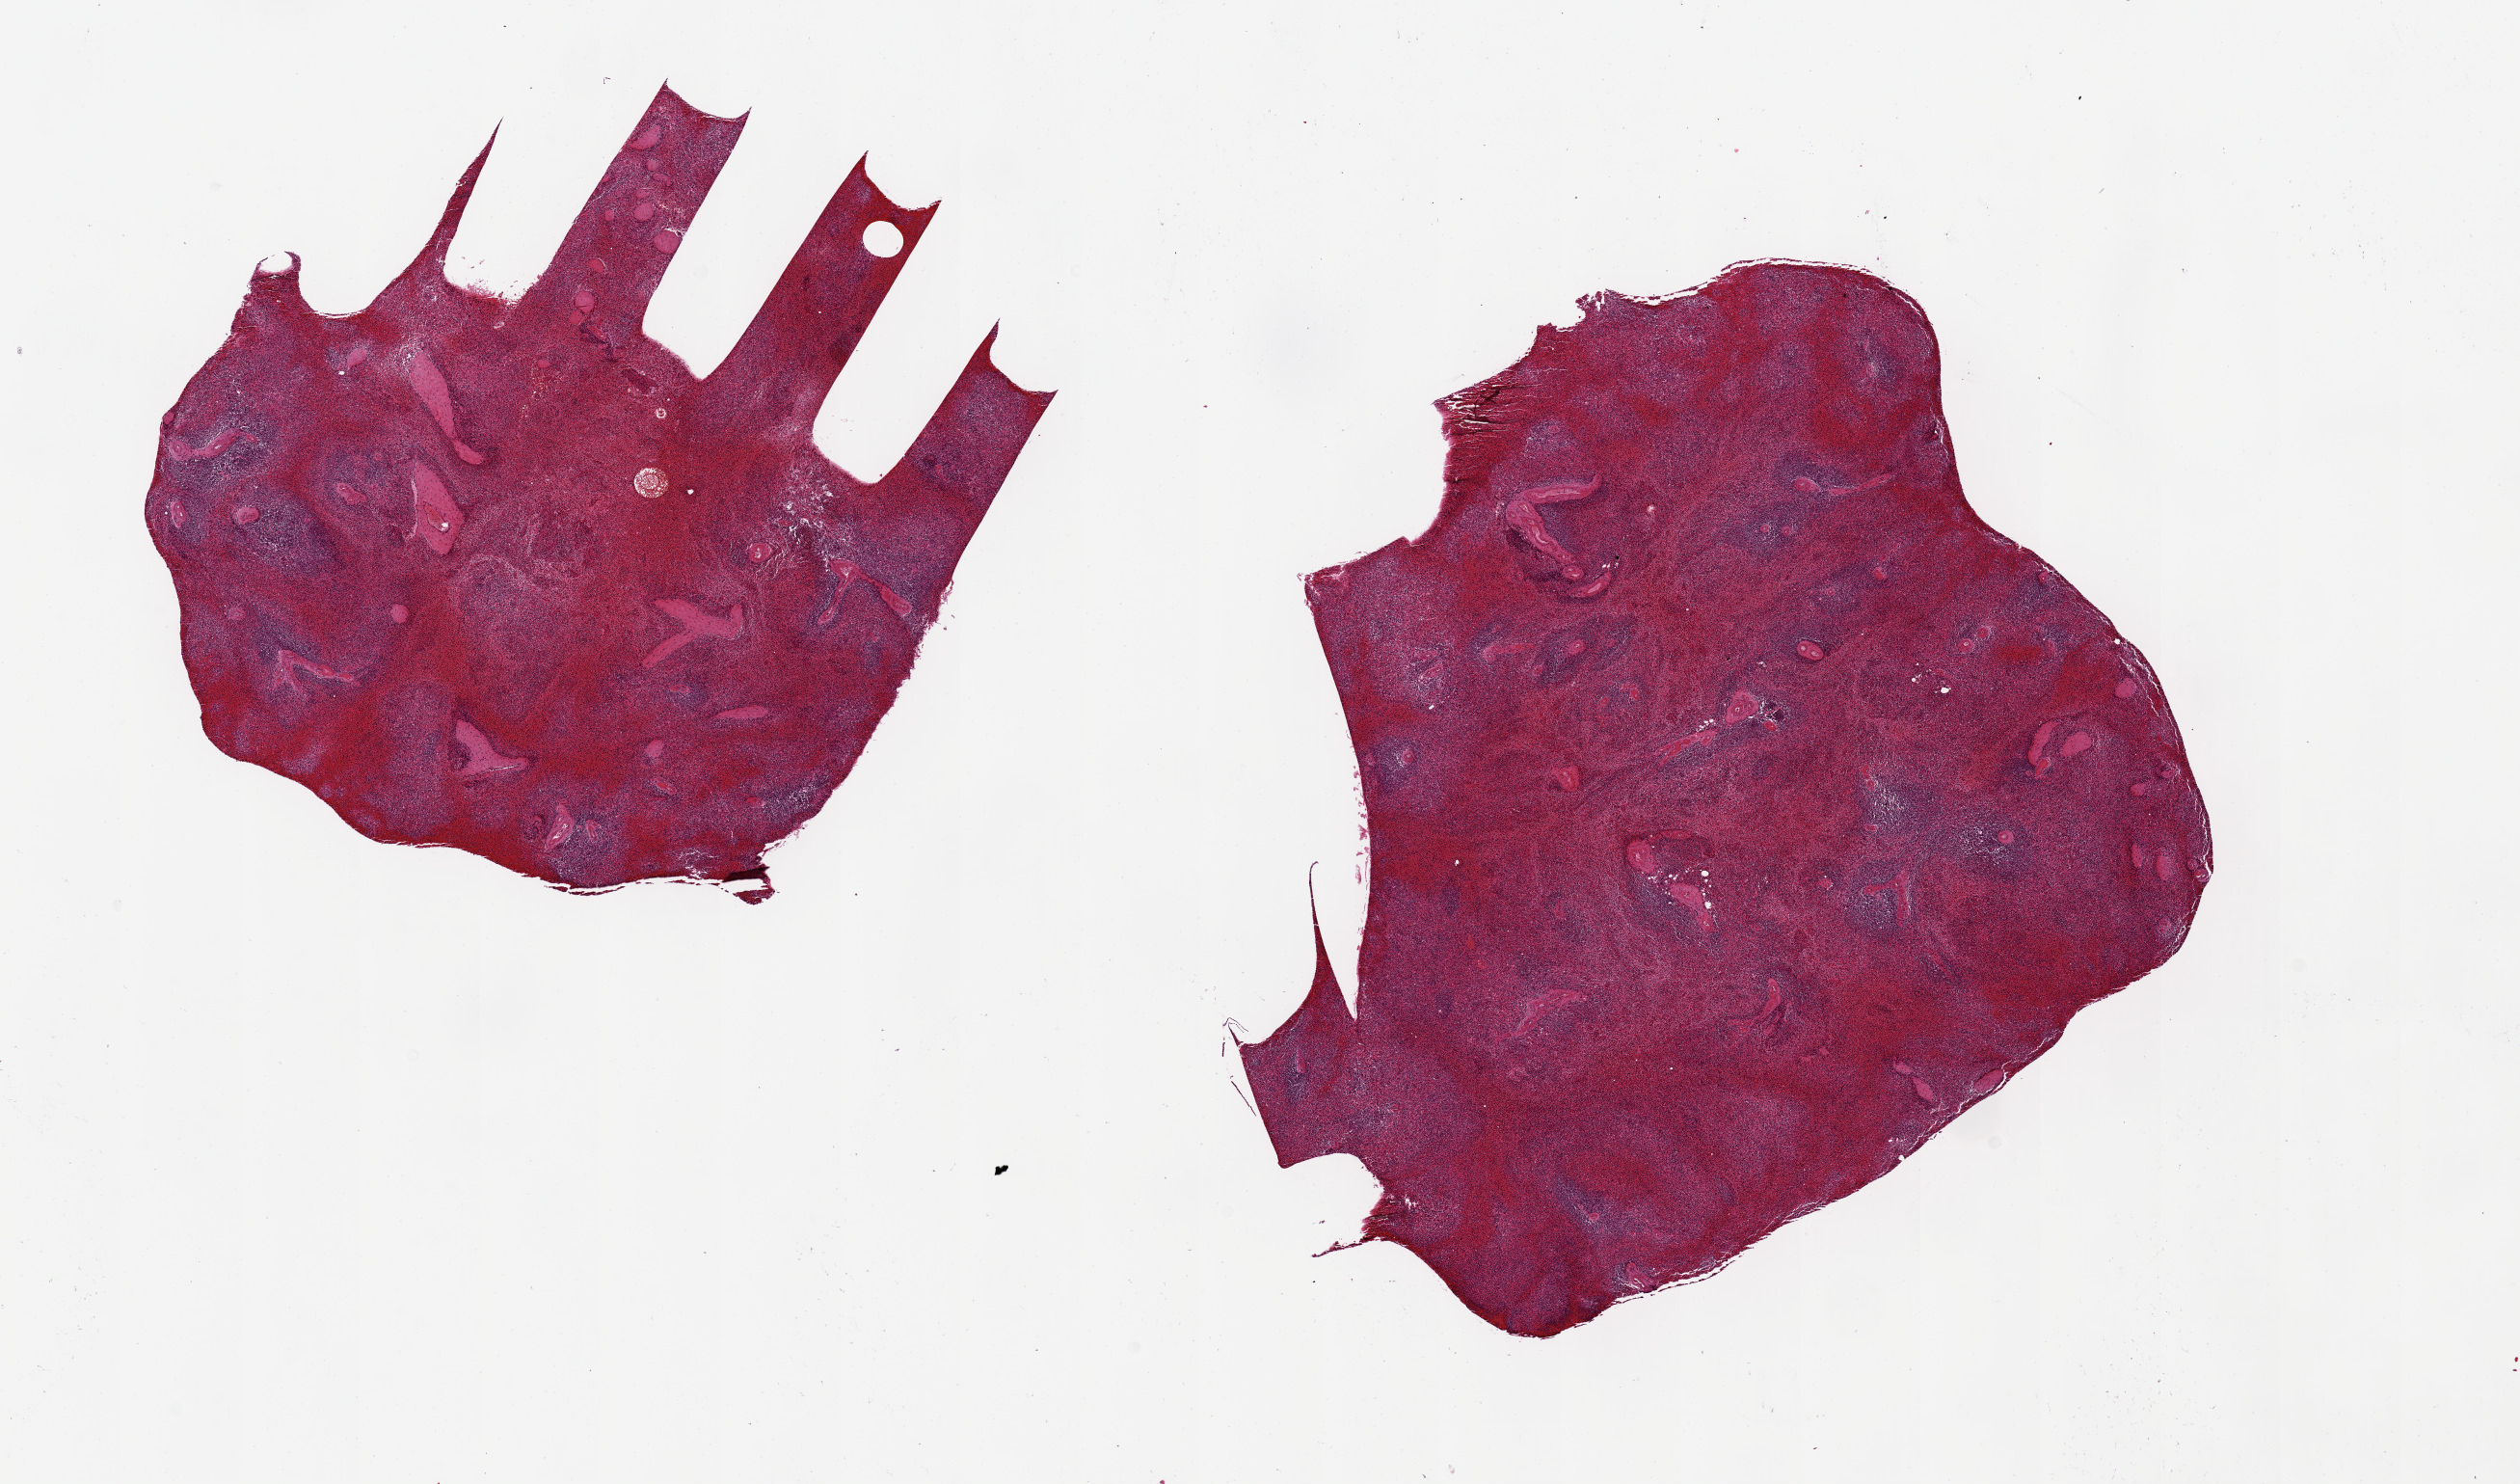
H&E whole-slide image — whole scanned area (about 20.7 x 12.2 mm) shown as a low-resolution overview; PAXgene-fixed paraffin-embedded (PFPE) section; sampled site (target tissue): spleen; tissue donor sample. Donor: male.
Reviewer comment on this tissue sample: 2 pieces, 7x6 & 8x7mm; Moderate congestion.